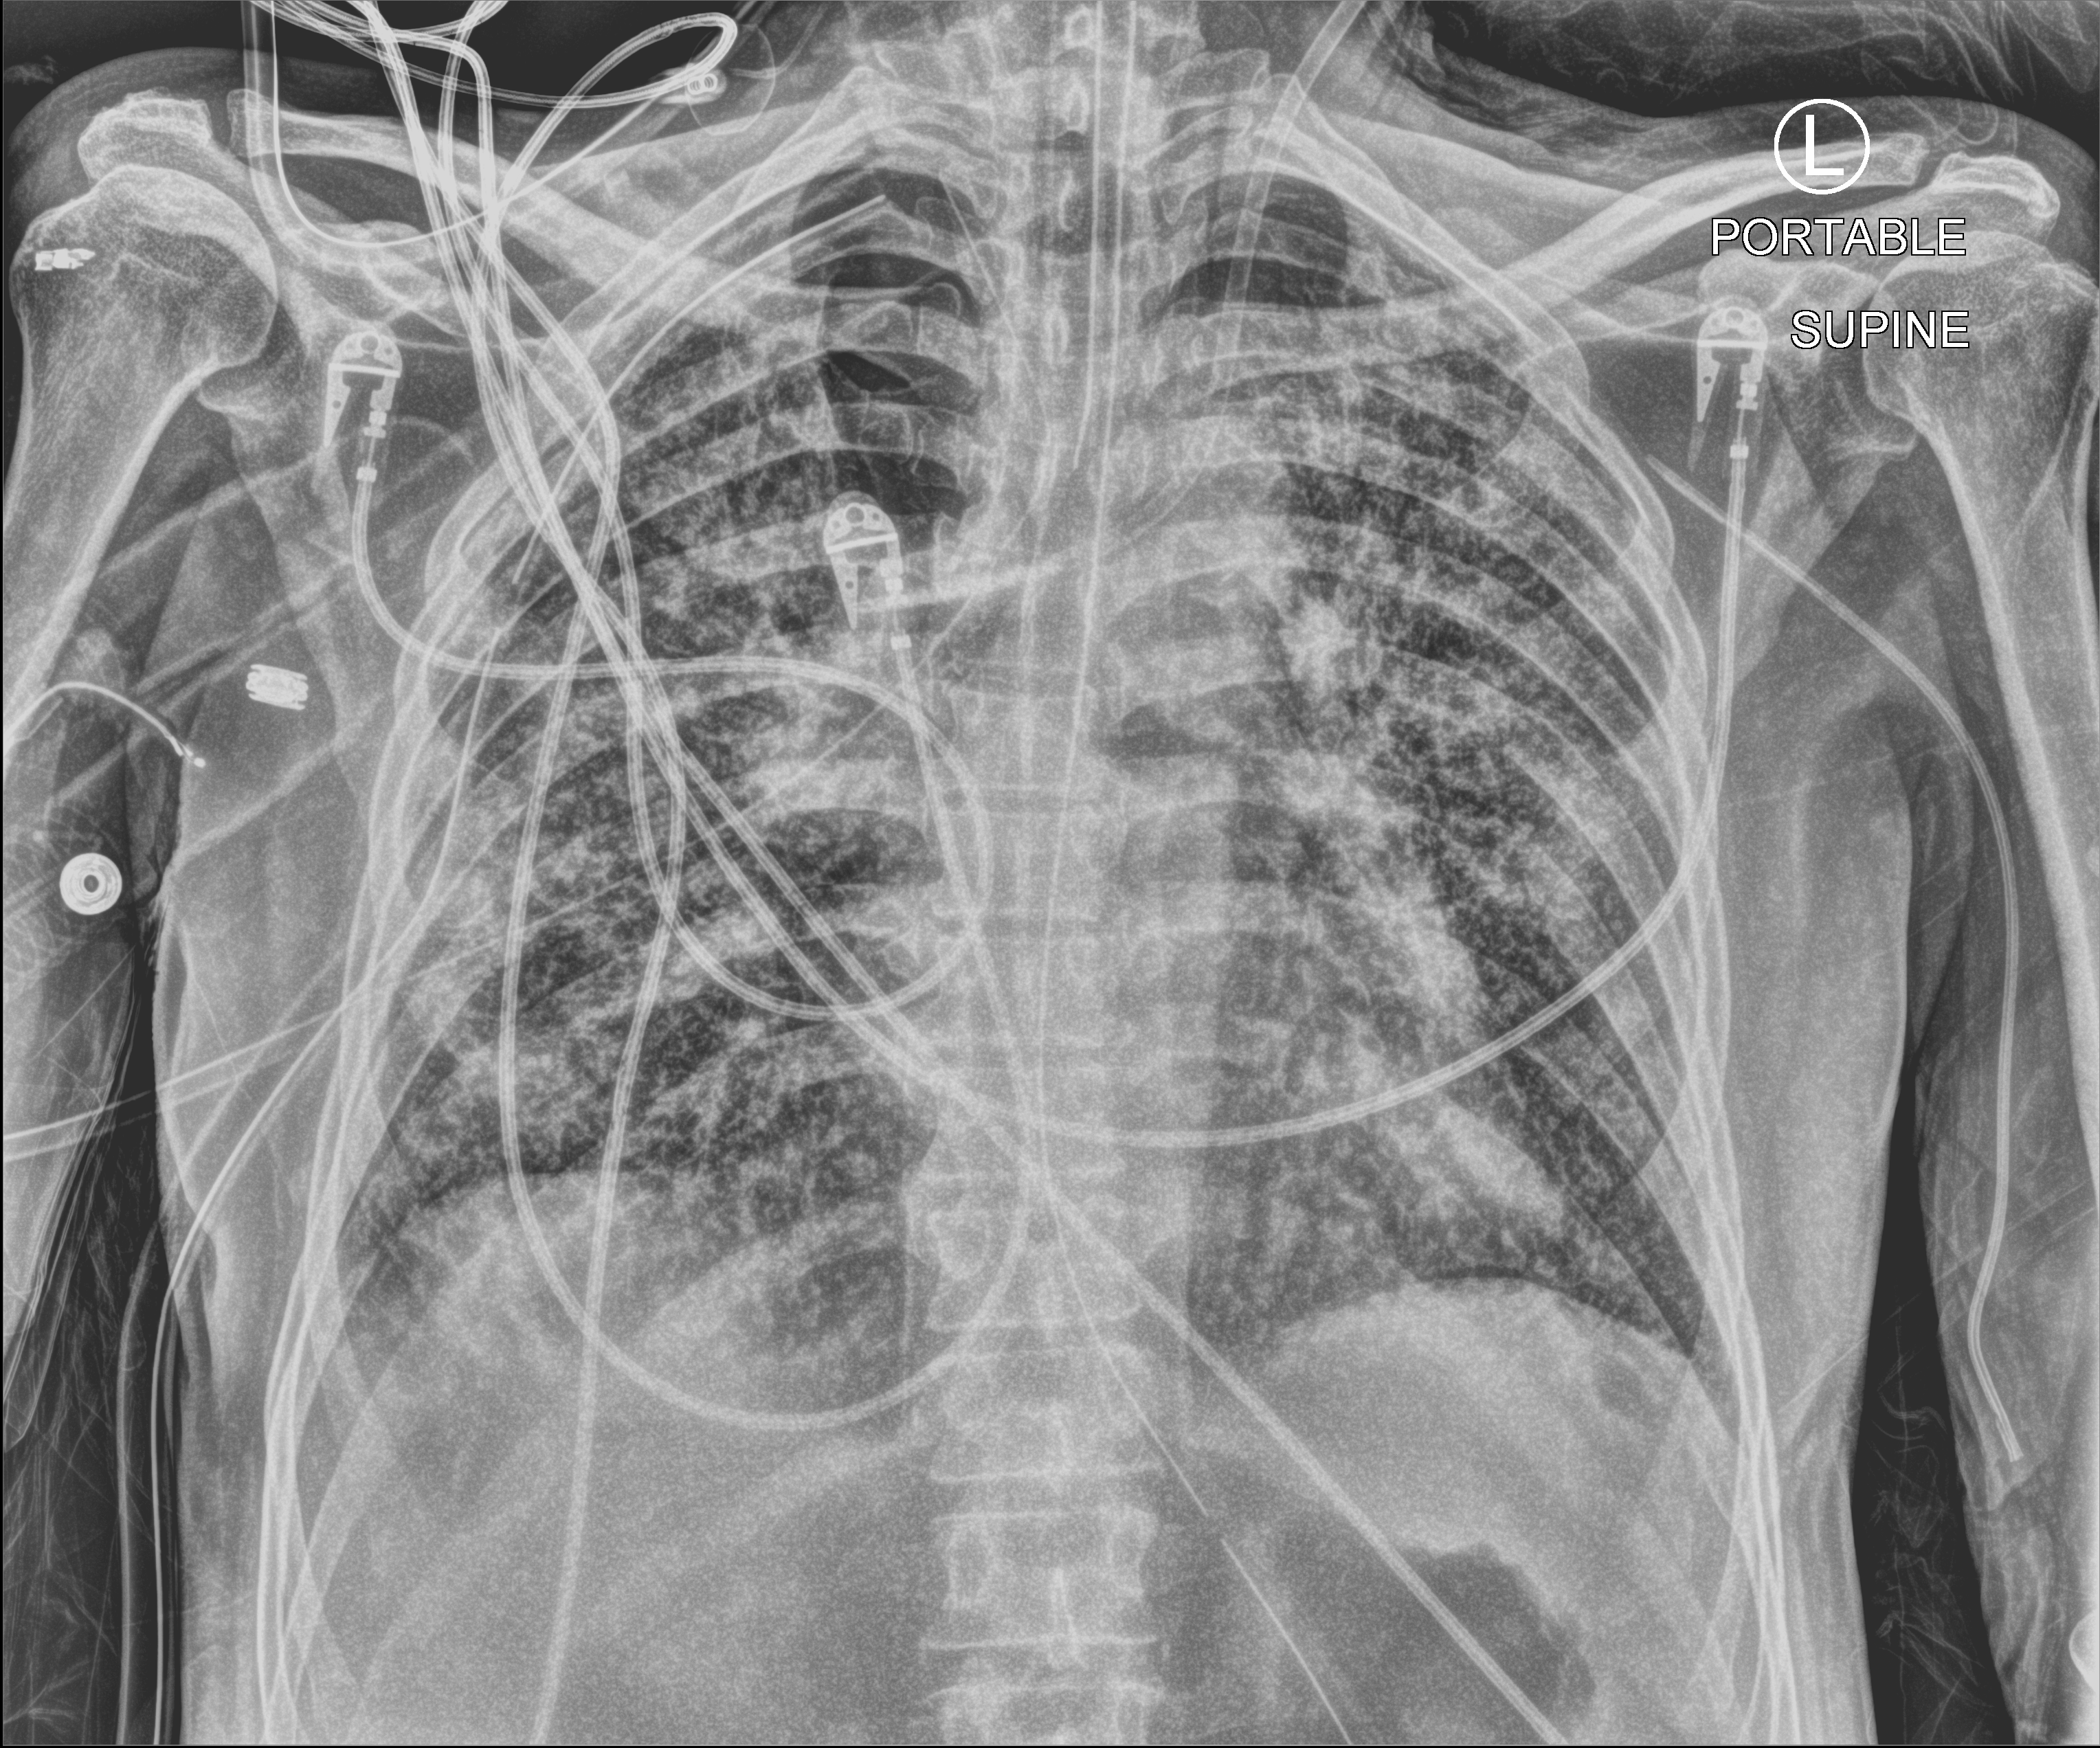
Portable chest radiograph, anteroposterior (AP) projection. Patient hospitalised with COVID-19; male, aged 60–74 years.
Hospital-stay facts (about this admission, not read from this image; timing relative to this image not recorded): mechanically ventilated during this hospital stay: yes; other chronic lung disease (admission record): yes.